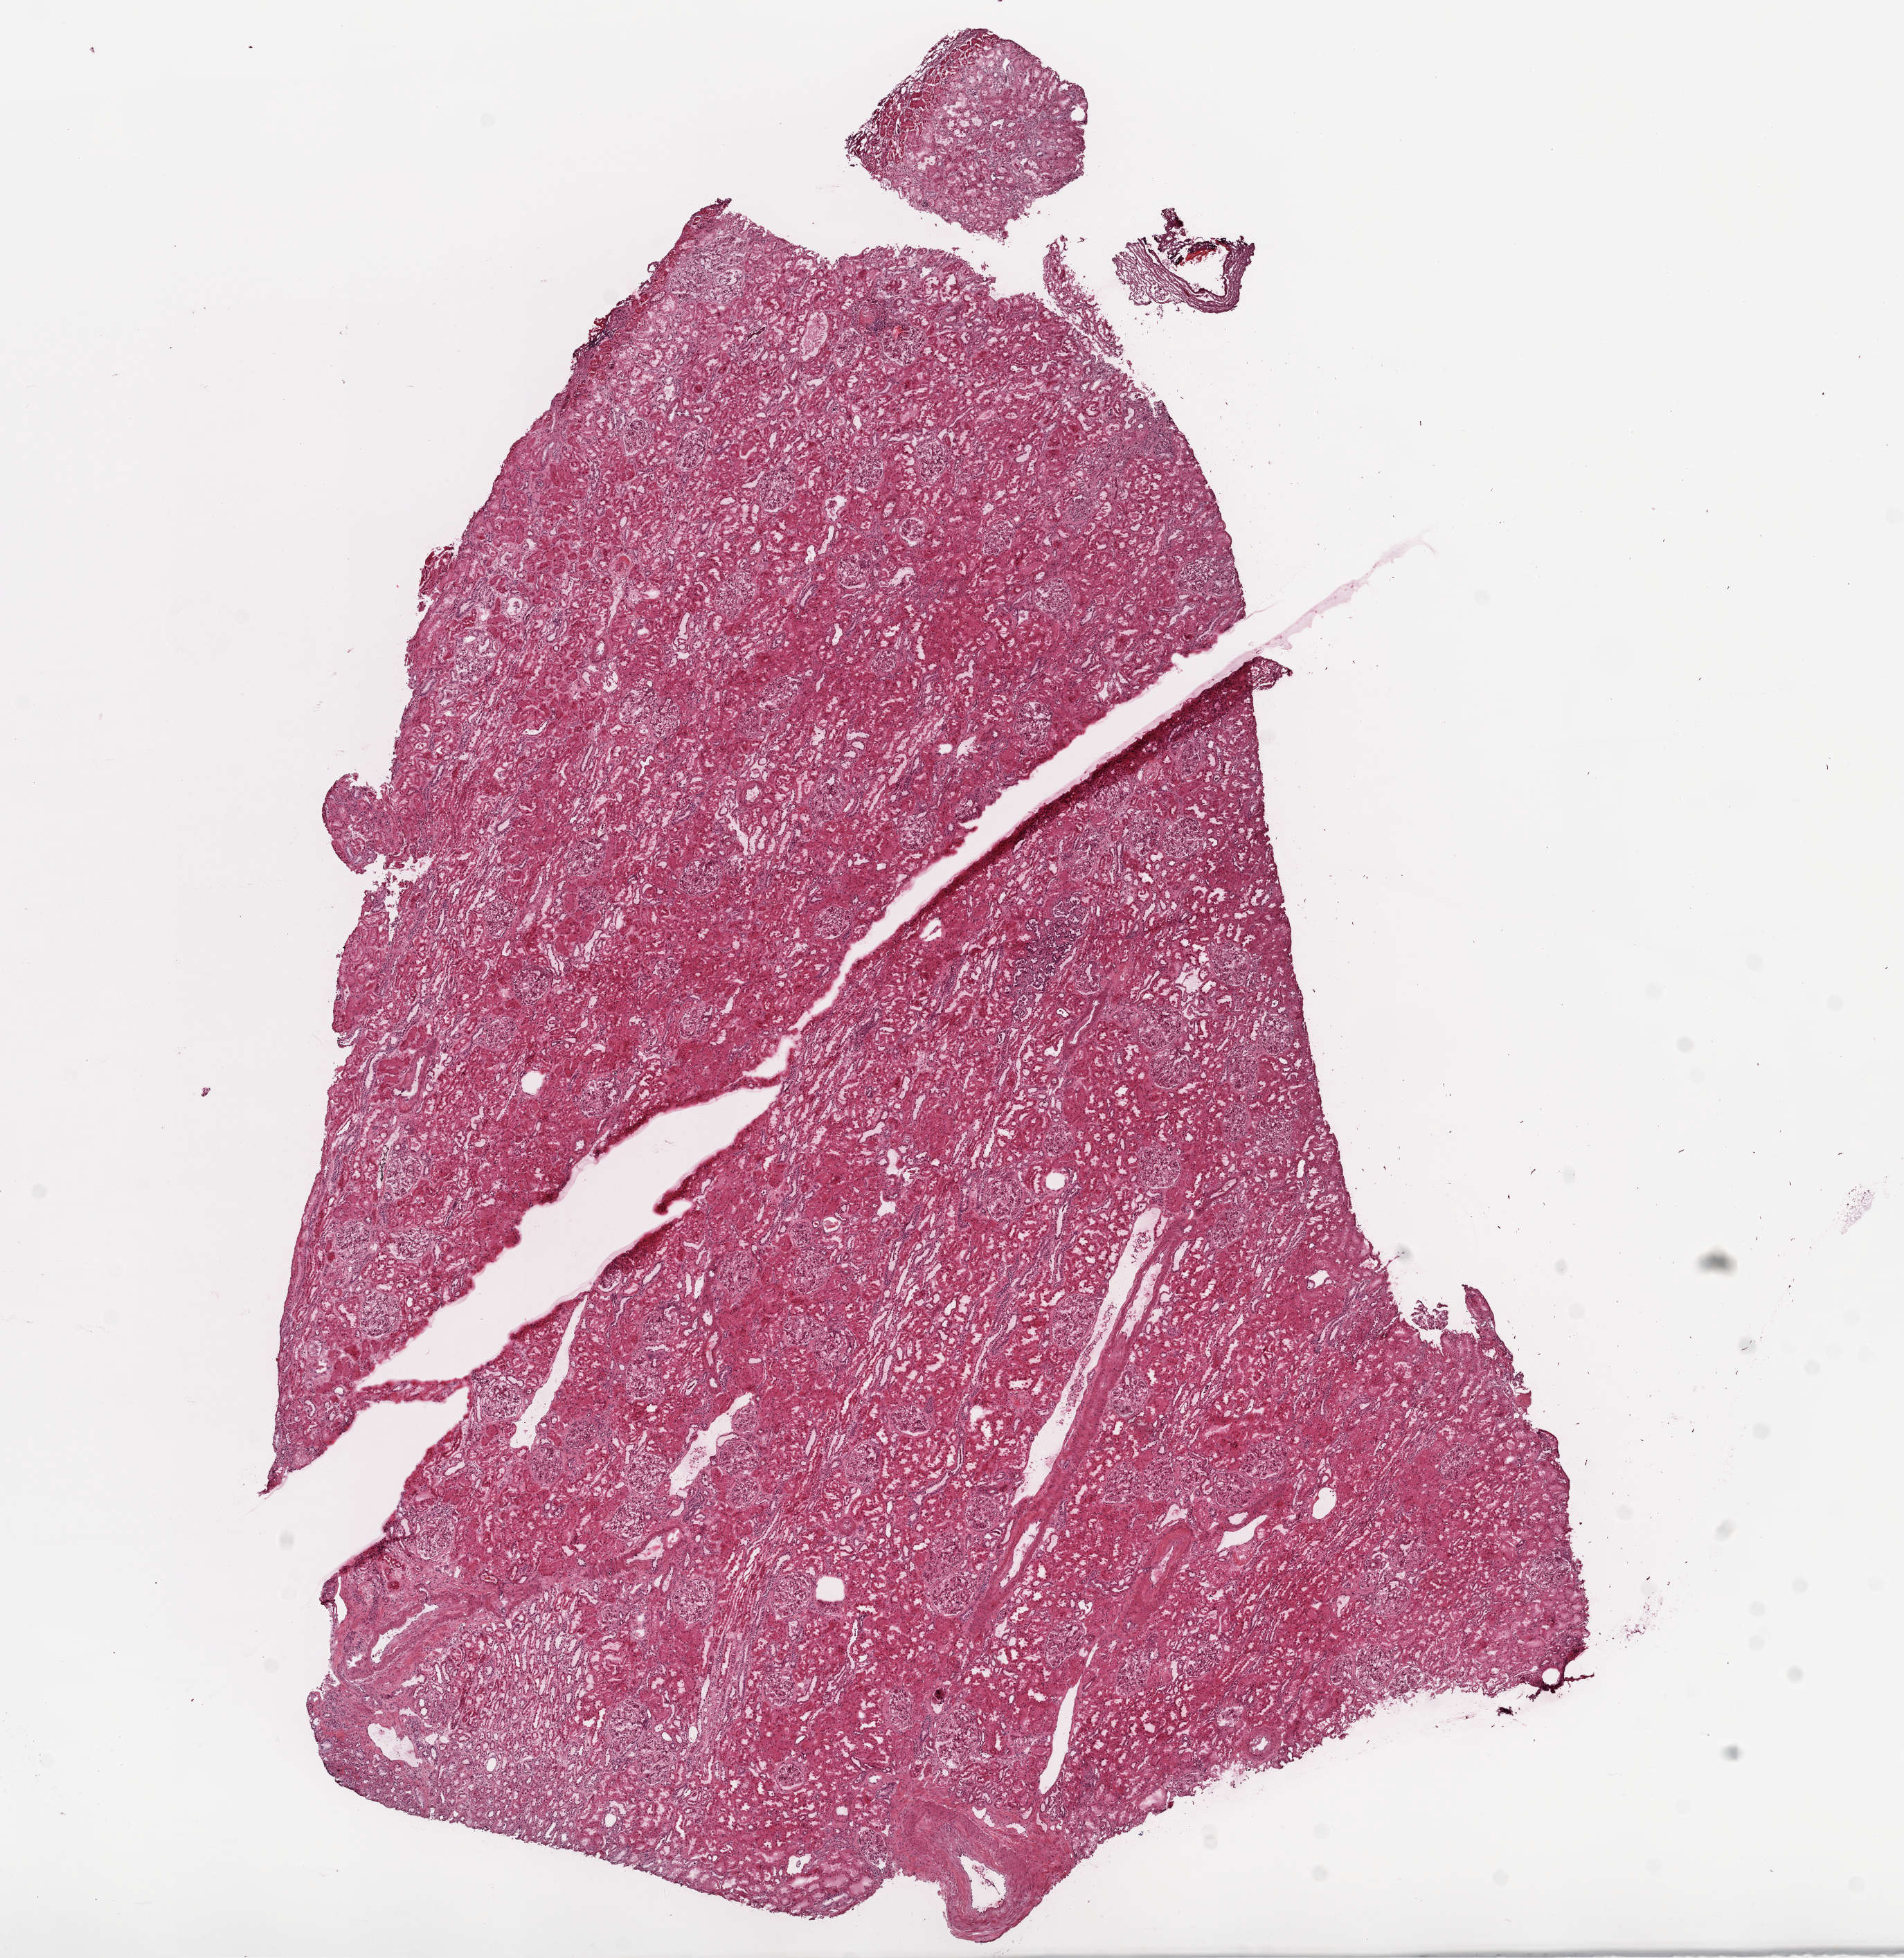
Whole-slide histology image, H&E-stained, low-resolution overview of the scanned area, about 11.0 x 11.3 mm (from a 20x scan). Frozen section from the top of the tissue portion. Sample: solid tissue normal (non-tumour tissue), kidney. Male, age 50 years at initial diagnosis.
- this section: solid tissue normal sample (biorepository sample class)
- patient diagnosis: Clear cell adenocarcinoma, NOS